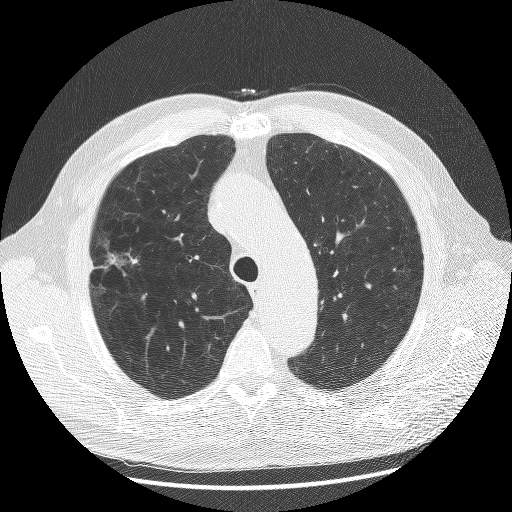
Axial slice from a low-dose chest CT screening exam, first (baseline) screen, lung window (W 1500 / L -600 HU), 2.5 mm slice thickness, 120 kVp, 512 × 512 image matrix, field of view 380 × 380 mm. Male participant, aged 70 years at enrolment. Current smoker at enrolment.
Expert-annotated lung lesion, bounding box (x1, y1, x2, y2) in pixels: (79, 230, 146, 305). The screening reader recorded 2 non-calcified nodules or masses ≥4 mm on this exam (left upper lobe, right upper lobe); which of them this box marks is not recorded. Later outcome: lung cancer diagnosed 23 days after this screen — non-small cell carcinoma, right upper lobe, poorly differentiated (G3), stage IA (AJCC 6th edition), 20 mm at pathology.